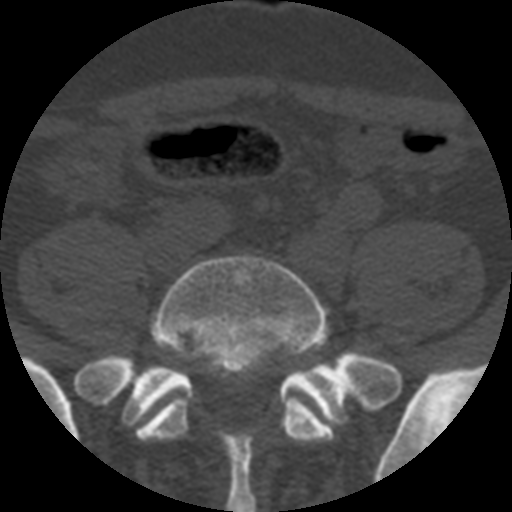
CT including the spine, one axial slice; position 54 of 508 along the scan axis; 120 kVp; bone window (W 1800 / L 400 HU); 512 × 512 image matrix, field of view 160 × 160 mm. Patient age 57 years. From the clinical record (not read from this slice): primary cancer: prostate.
Annotated regions visible in this slice (semi-automatically segmented with operator editing):
- L5 vertebra: bounding box [x1, y1, x2, y2] px = [136, 254, 389, 444]